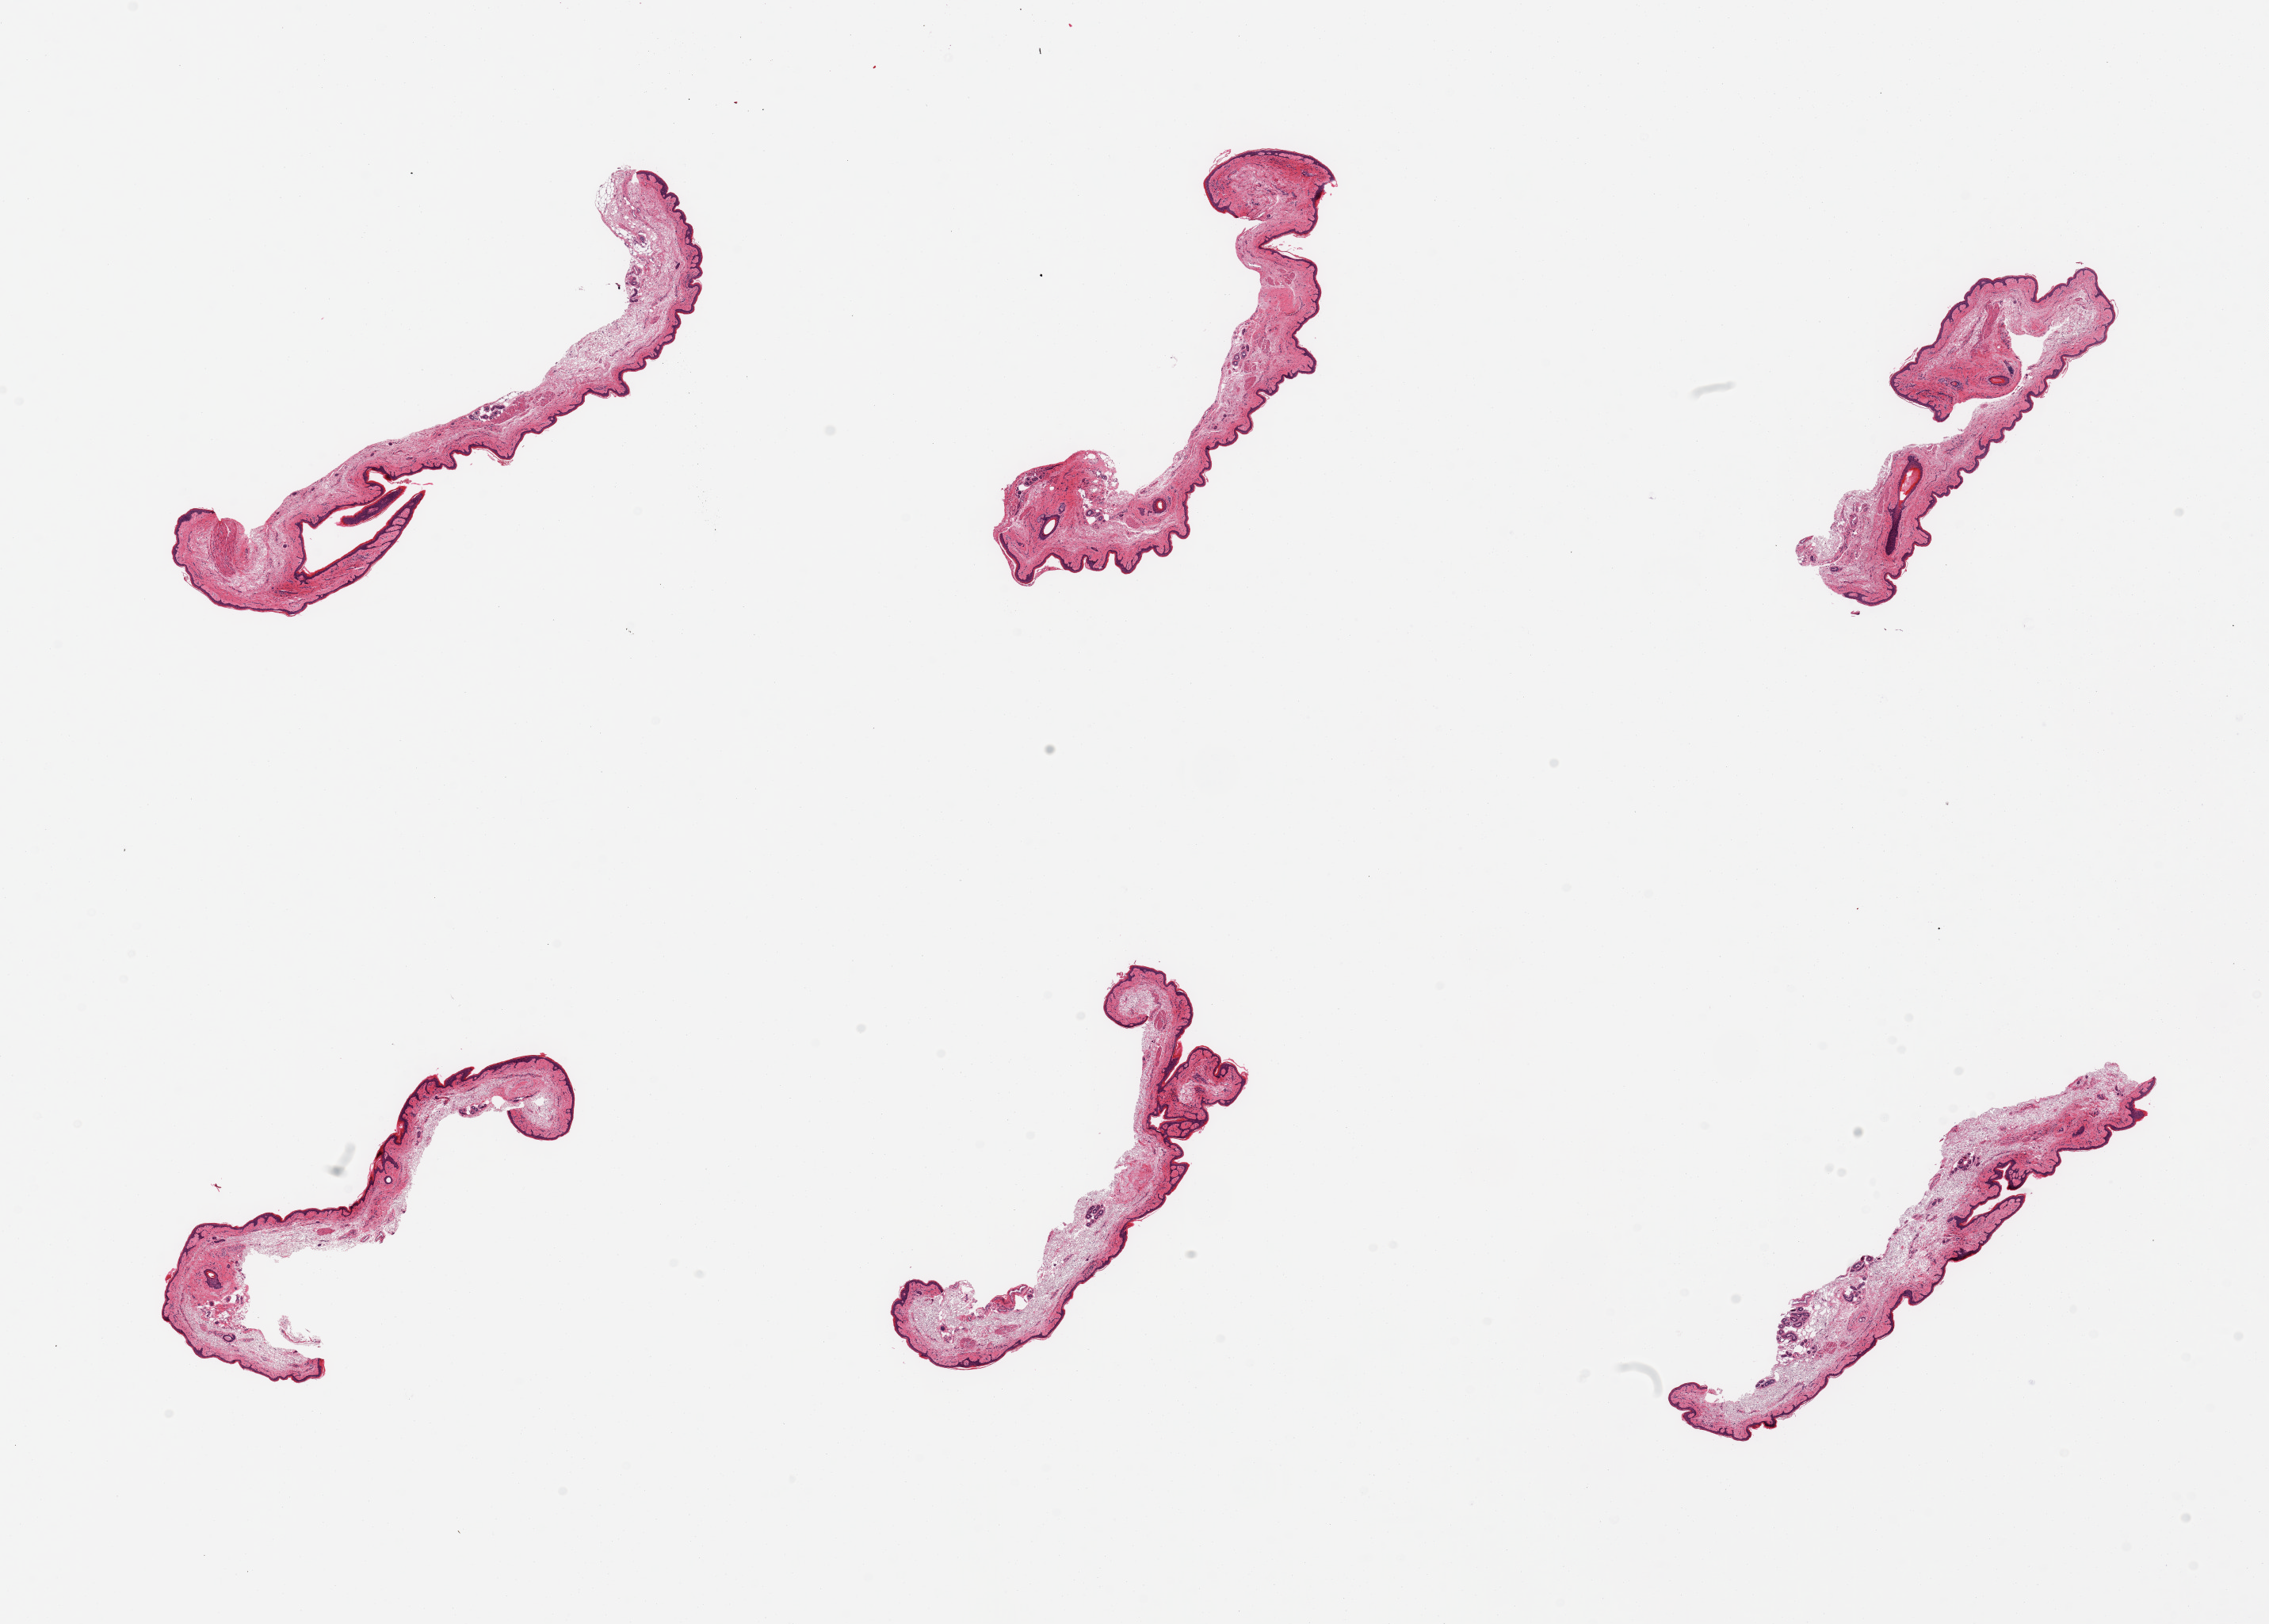
Whole-slide image, haematoxylin and eosin stain, brightfield, whole scanned area (about 22.6 x 16.2 mm, acquisition: 20x scan) shown as a low-resolution overview; PAXgene-fixed paraffin-embedded (PFPE) section; section of skin of suprapubic region (target tissue); tissue donor sample. Donor sex: female.
Pathologist's review note for this sample: 6 pieces; atrophic and edematous; well trimmed.